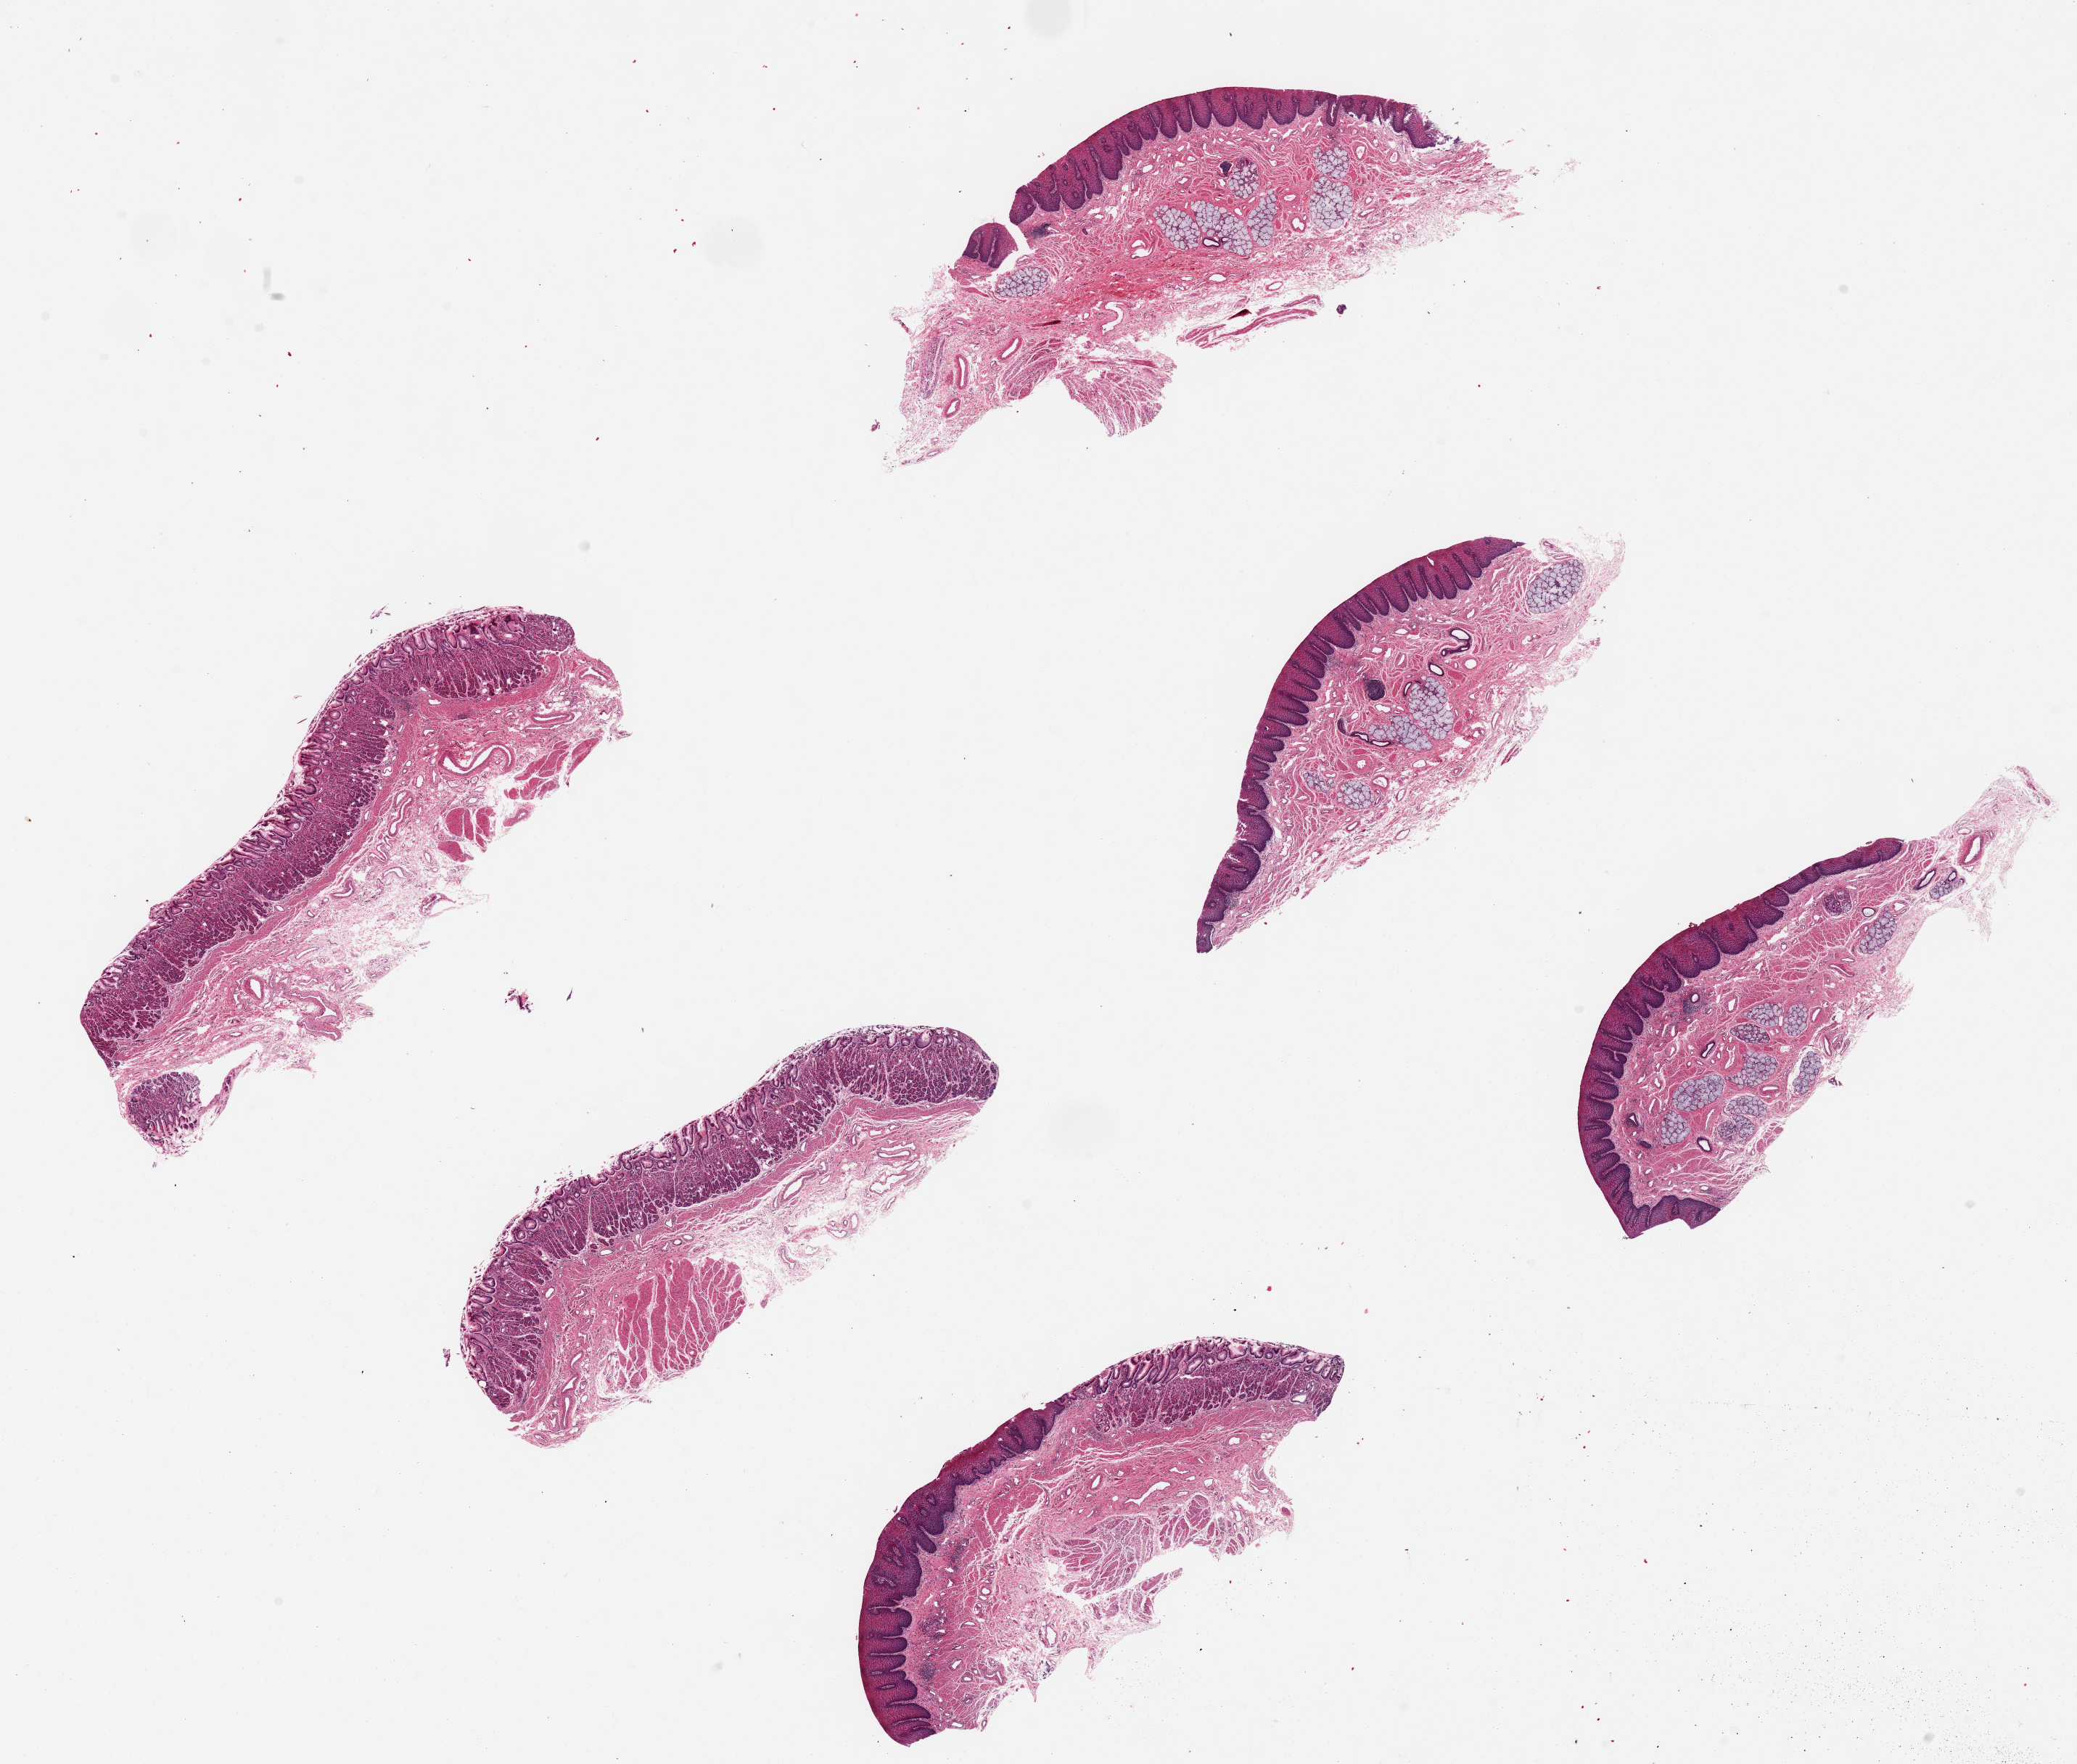
Digitized hematoxylin and eosin (H&E)-stained section — low-resolution overview of the scanned area, about 22.6 x 19.2 mm, PAXgene-fixed, paraffin-embedded tissue, sampled site (target tissue): esophageal mucous membrane, donor tissue sample.
Review note (as recorded): 6 pieces up to 6.7x2.8 mm??? 3 pieces with hyperplastic squamous epithelium, 2 with fundic-type glandular epithelium; 1 with glandular and squamous epi.; probable reflux changes; no intestinal metaplasia.